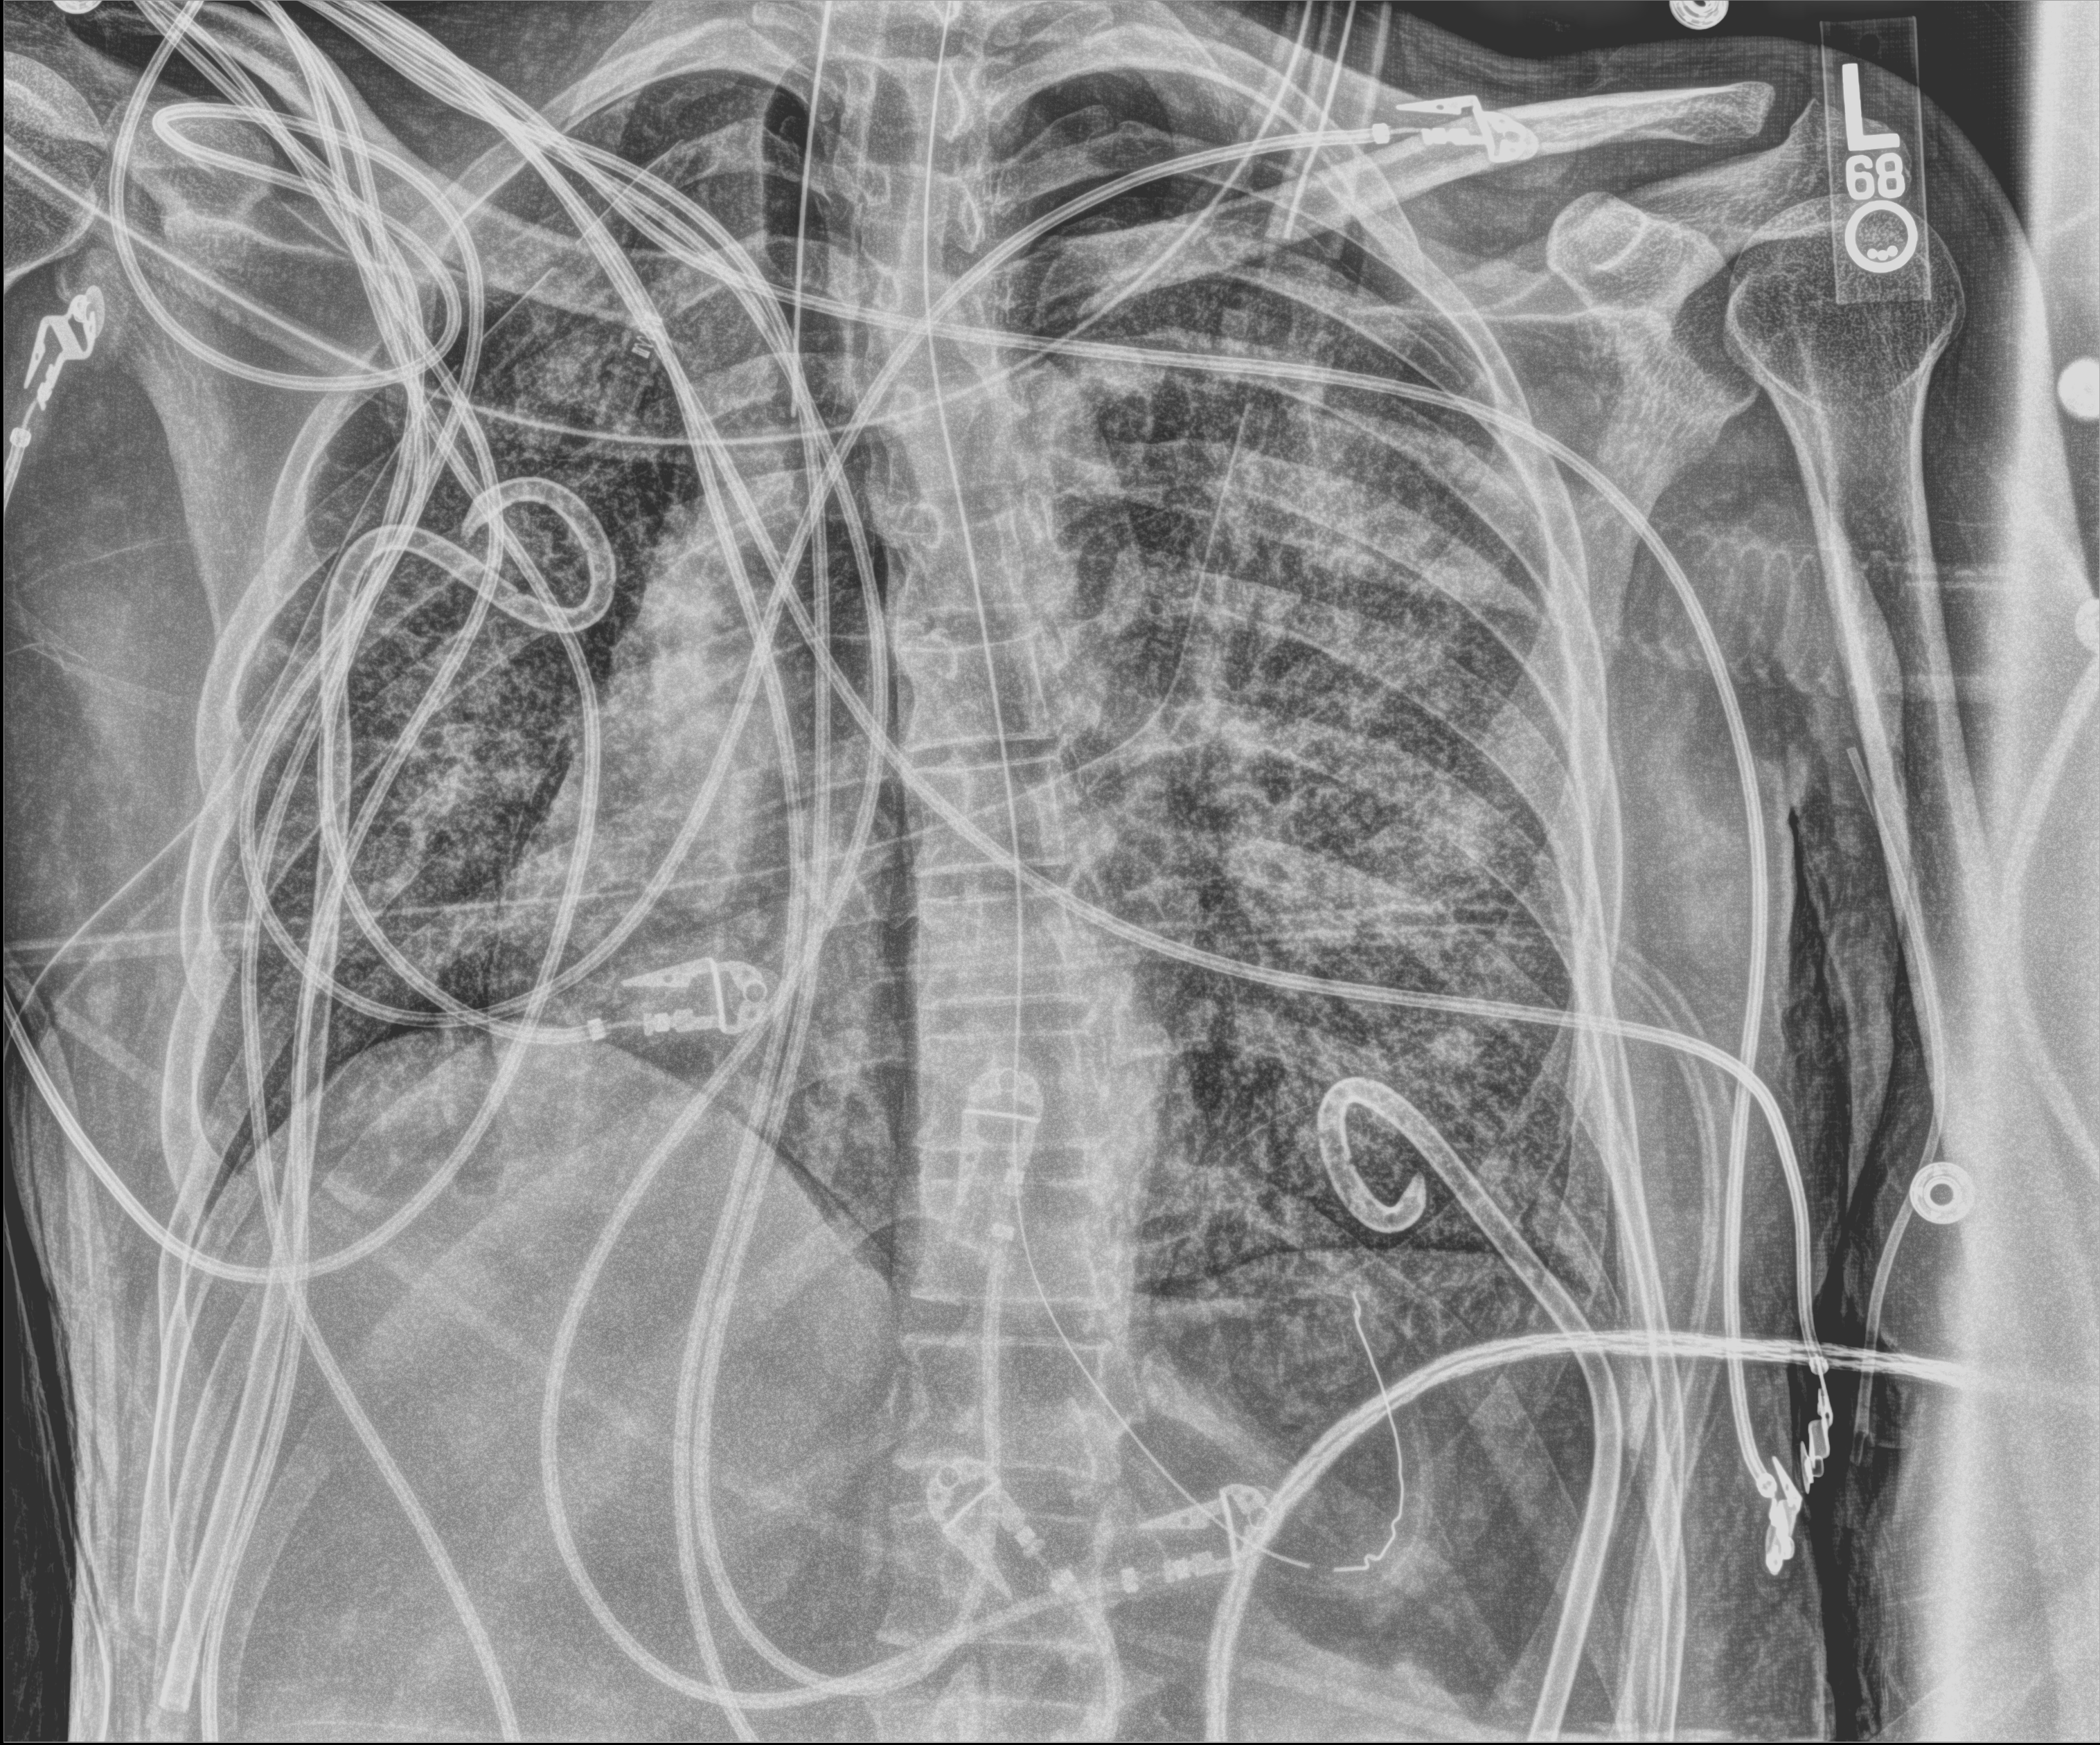
Chest X-ray (portable). Adult patient hospitalised with COVID-19, age 18–59 years.
Hospital-stay facts (about this admission, not read from this image; timing relative to this image not recorded): admitted to intensive care during this hospital stay: yes; mechanically ventilated during this hospital stay: yes.